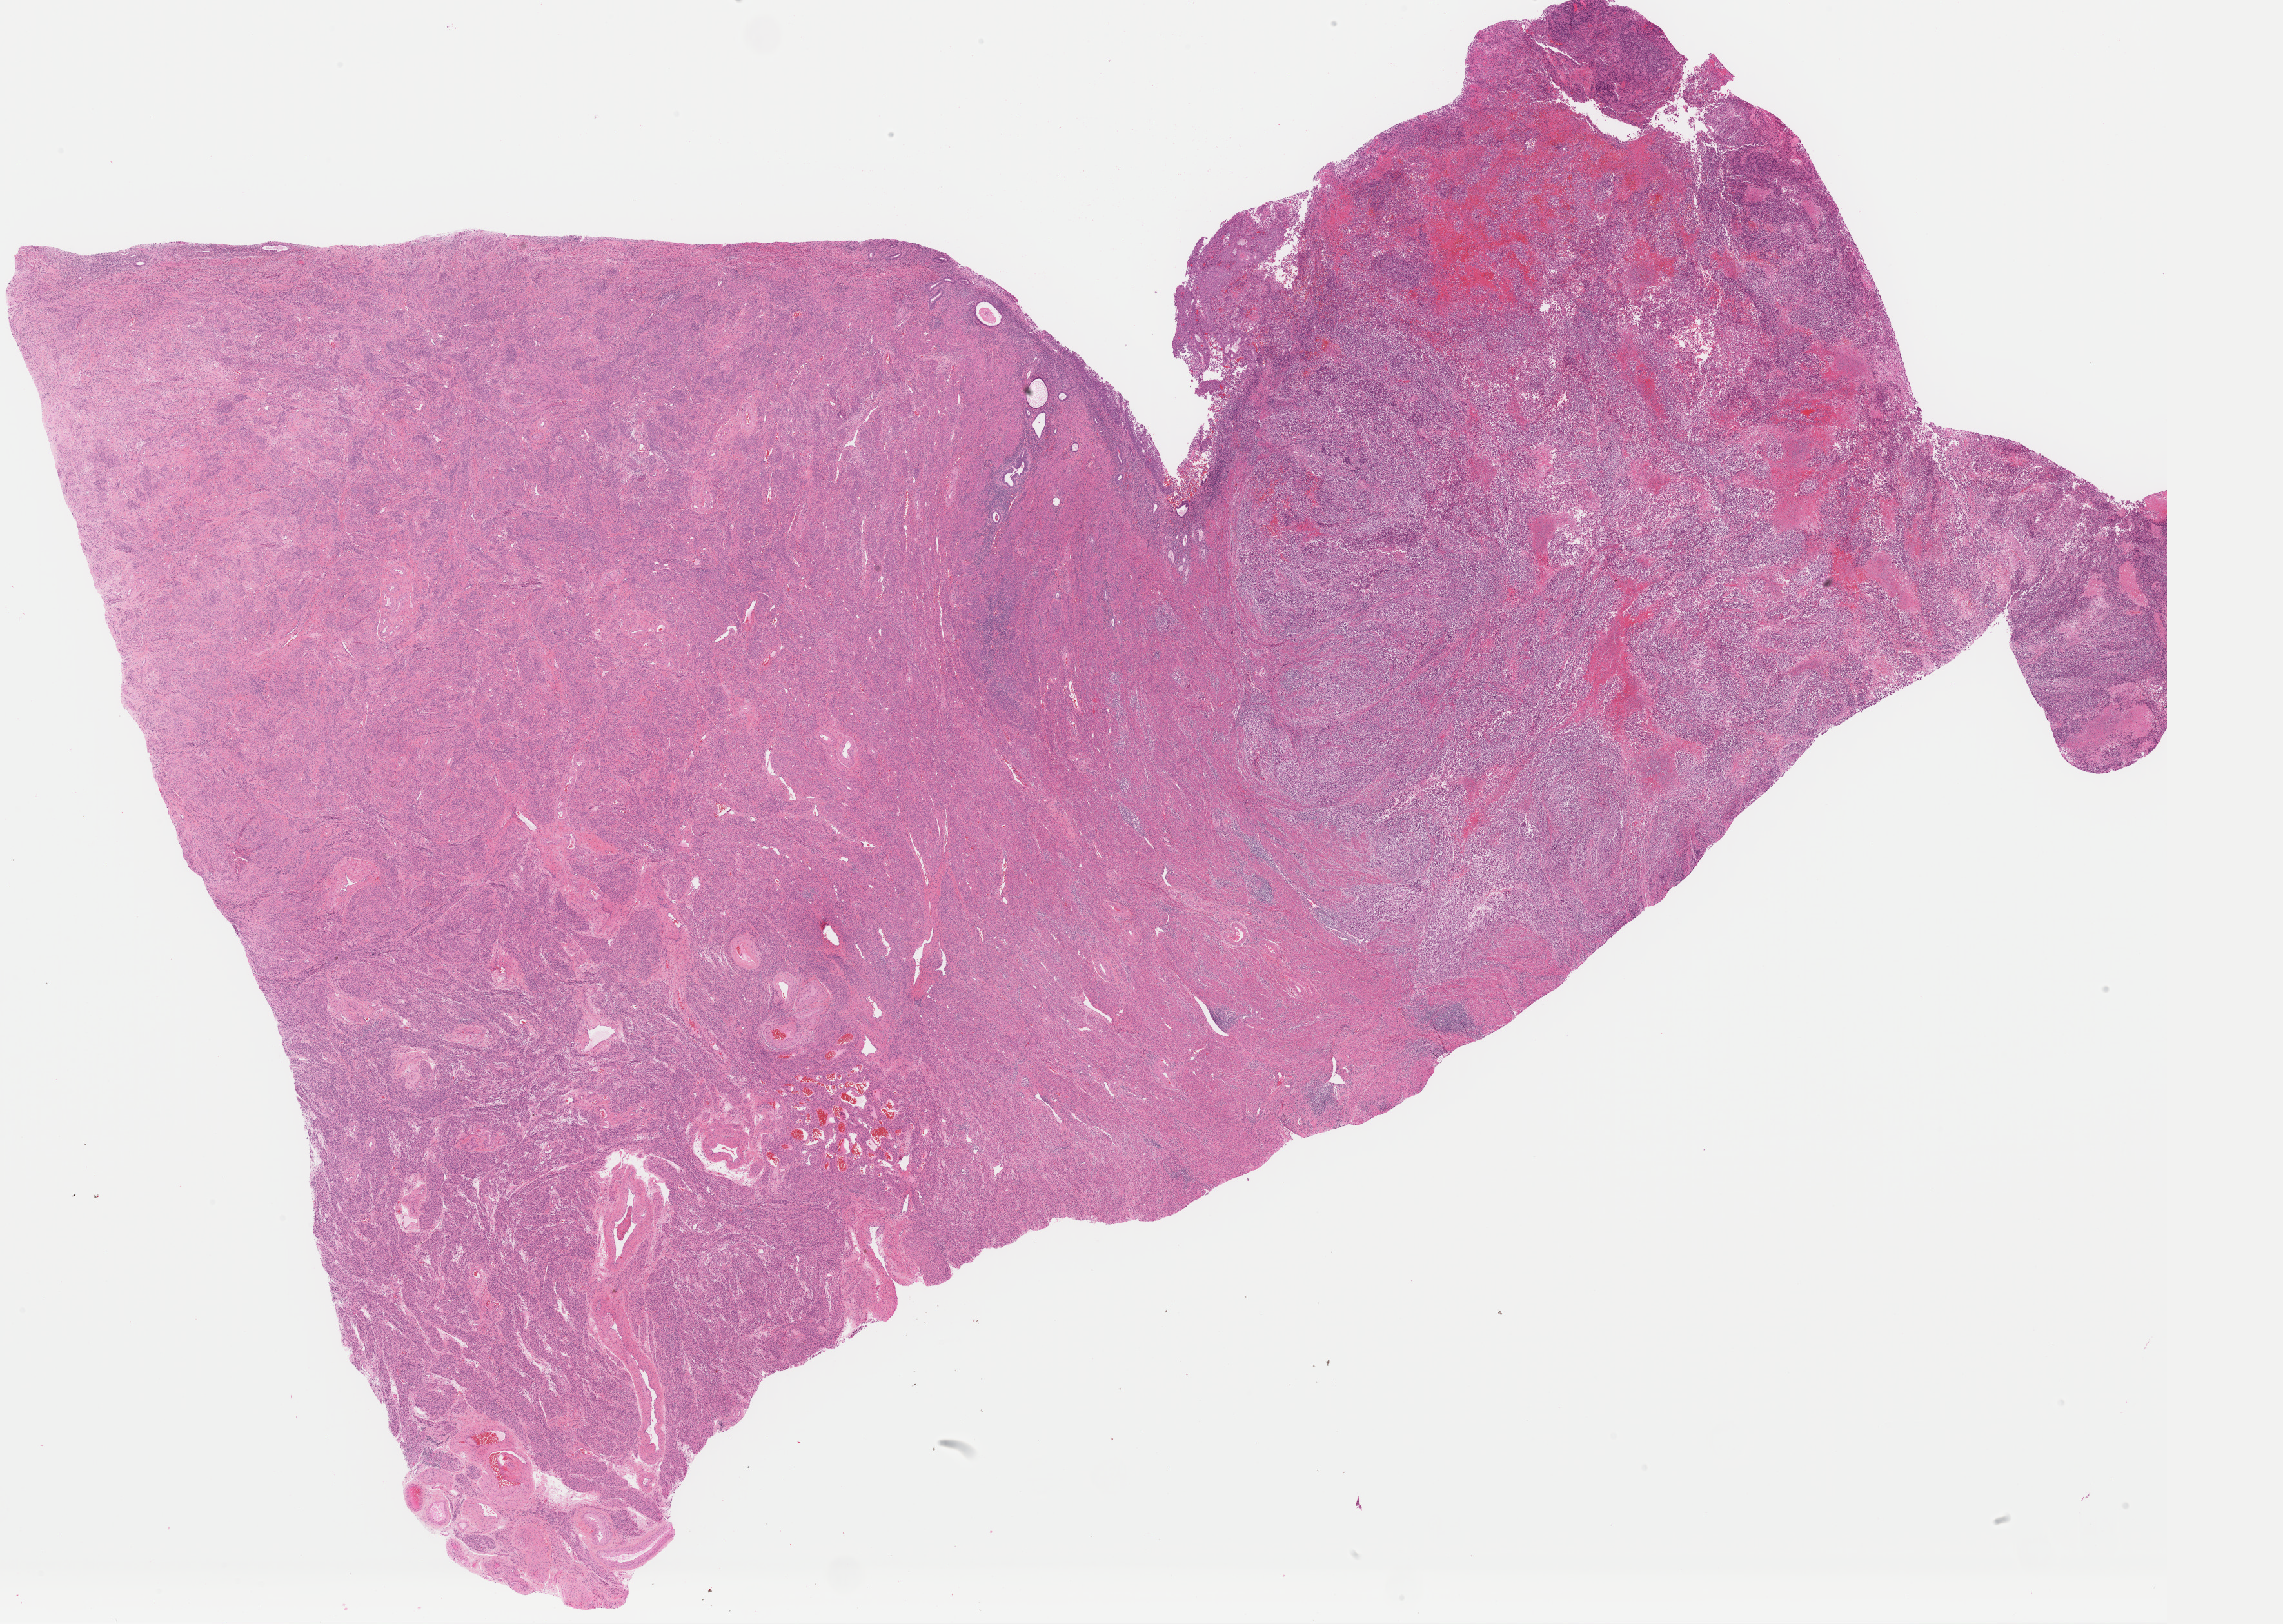
H&E-stained whole-slide image, low-resolution overview of the scanned area, about 28.0 x 19.9 mm (slide scanned at 40x); formalin-fixed paraffin-embedded (FFPE) diagnostic section; sample: primary tumour, uterus. Female, age 68 years at initial diagnosis. Histologic grade: G3 (poorly differentiated).
- FIGO stage: IA
- pathologic diagnosis: Serous cystadenocarcinoma, NOS